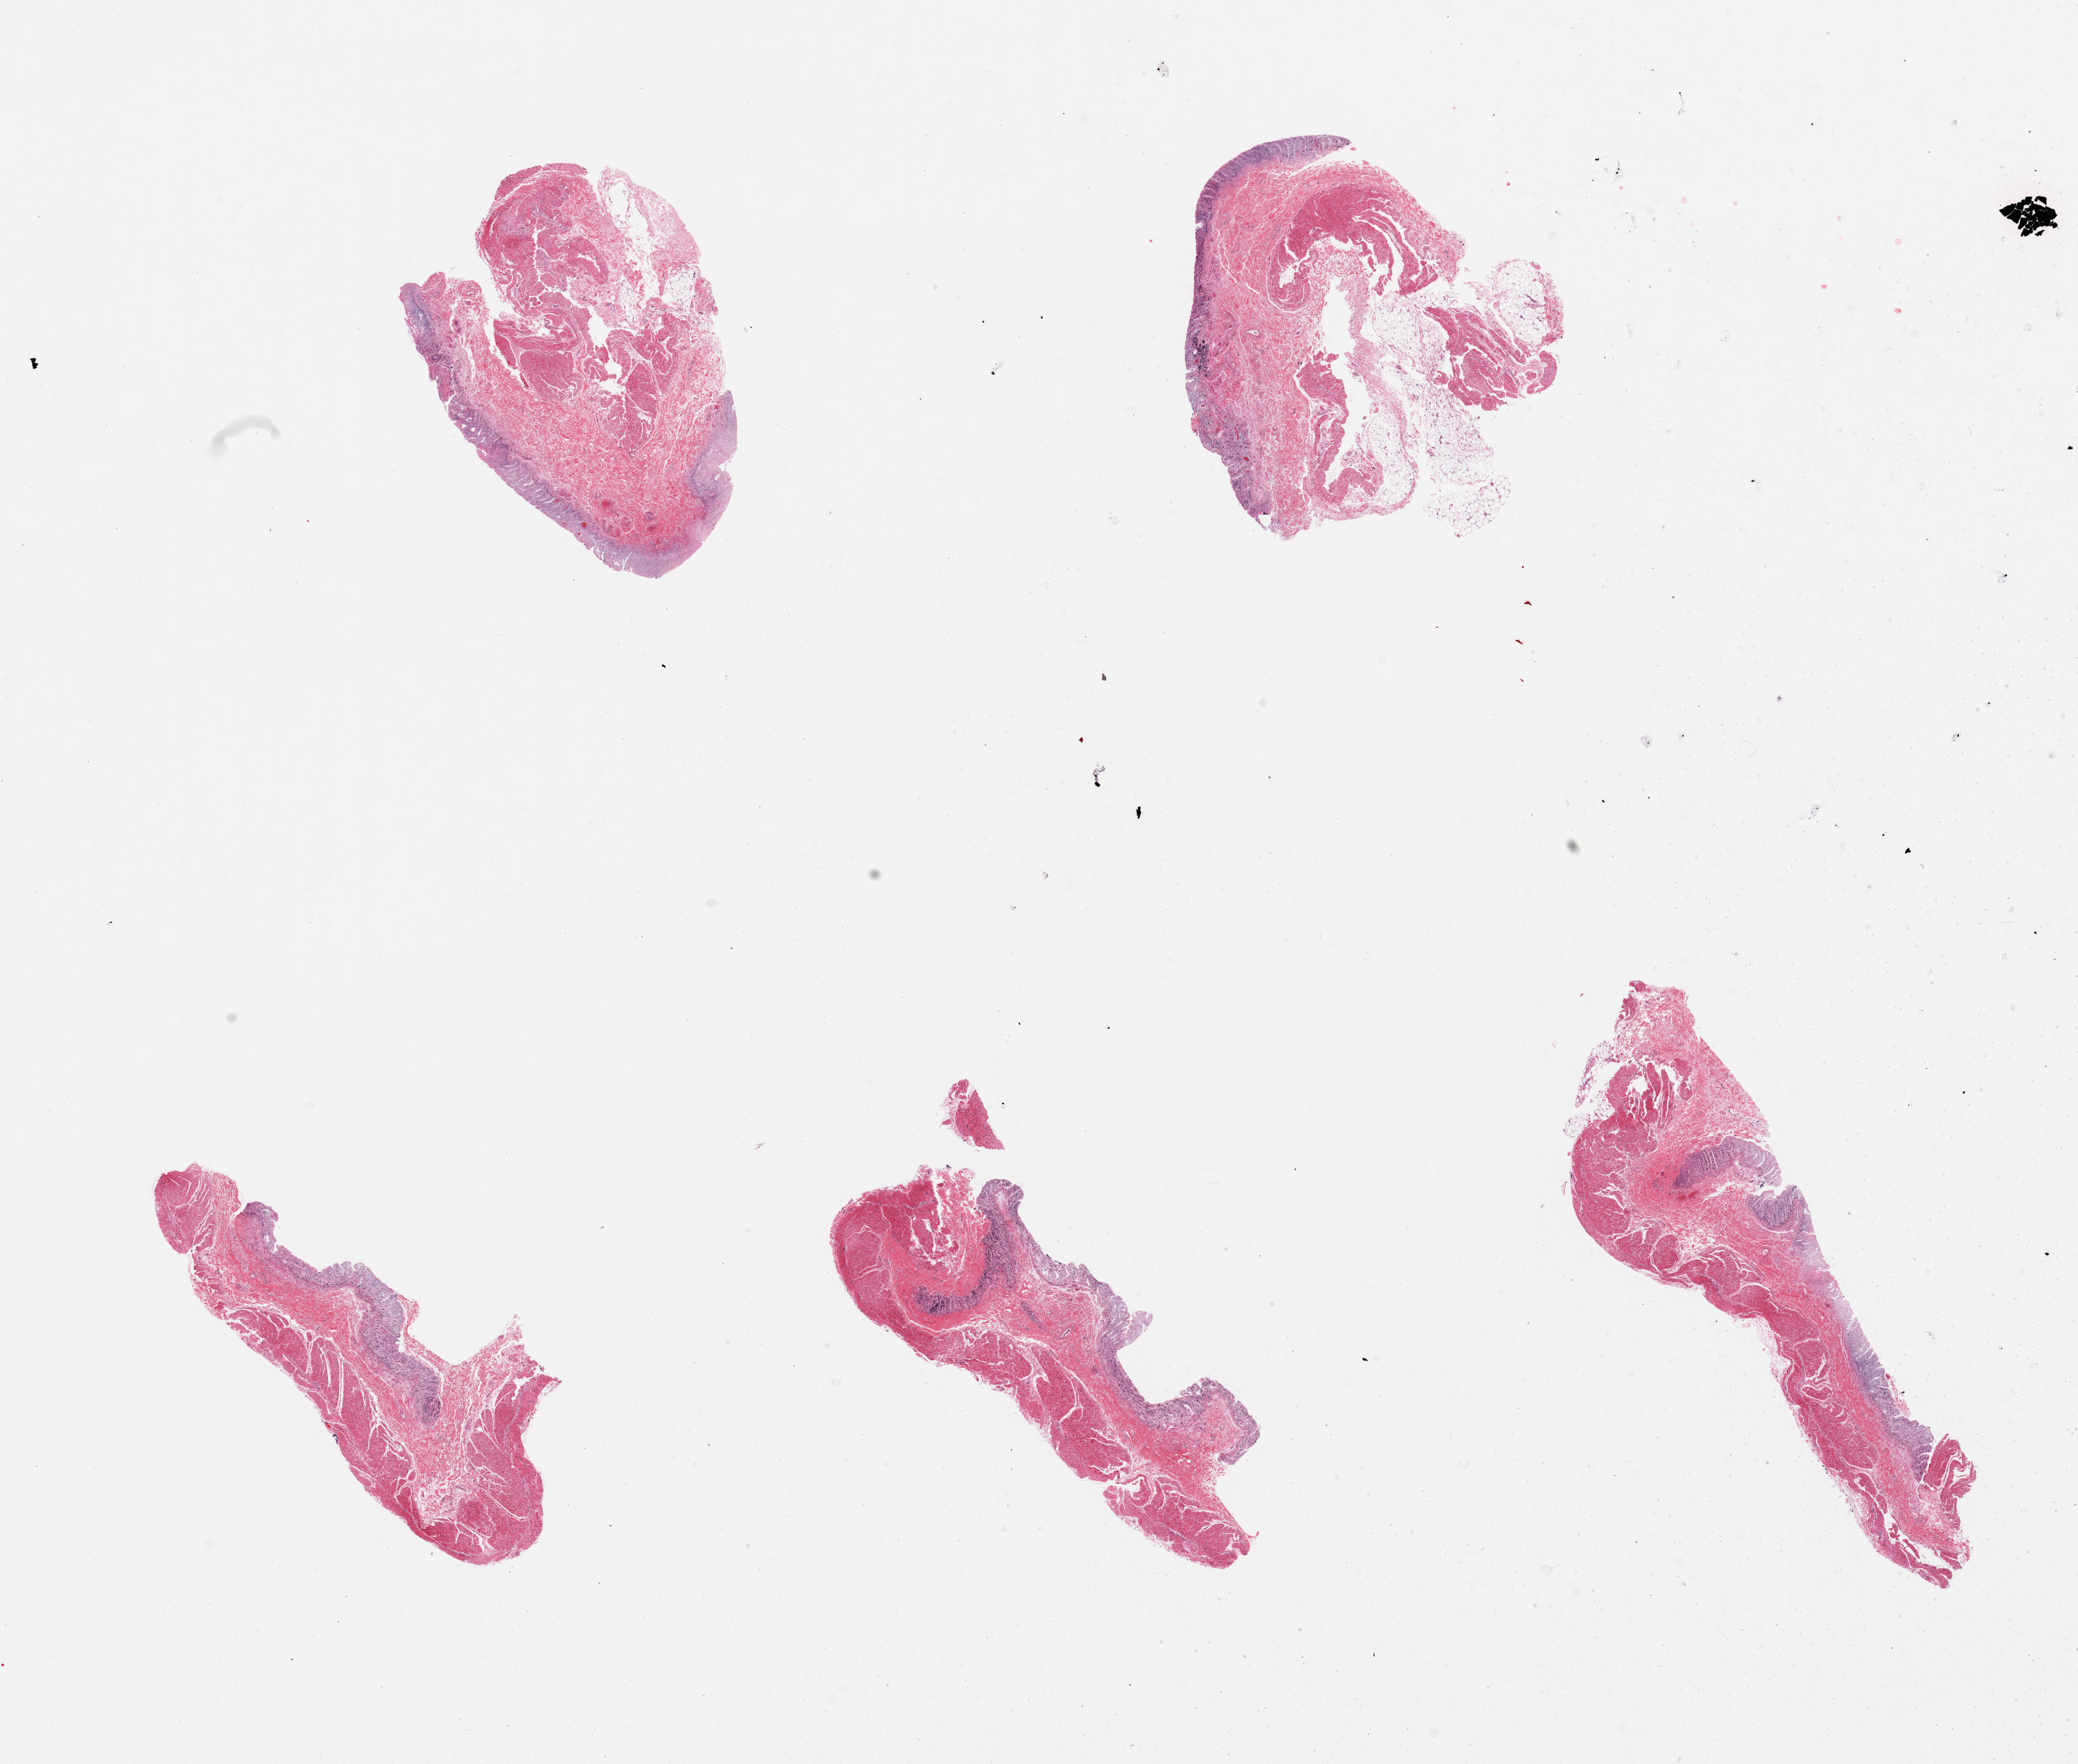
Digitized haematoxylin and eosin-stained section, brightfield, shown as a low-resolution overview of the whole scanned area (about 22.6 x 19.2 mm); PAXgene-fixed paraffin-embedded (PFPE) section; target tissue: transverse colon; tissue donor sample. Female donor.
Pathologist's review note for this sample: 5 pieces, mucosa totally autolyze/sloughed.